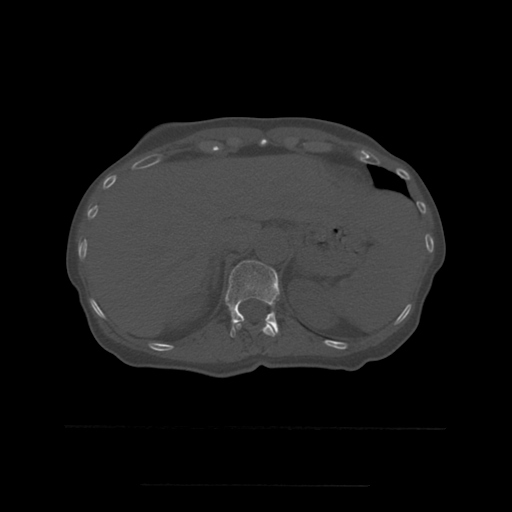
CT including the spine, one axial slice; slice 268 of 544 in the series (ordered by position); bone window (W 1800 / L 400 HU); 1.25 mm slice thickness; 512 × 512 image matrix, field of view 350 × 350 mm. Patient age 58 years. Case-level facts recorded for this patient, not image findings: primary cancer: lung.
Outlined on this slice (semi-automatic segmentation, software-assisted and operator-edited):
- T11 vertebra: bounding box (x1, y1, x2, y2) in pixels: (232, 321, 276, 338)
- T12 vertebra: (225, 261, 280, 338)